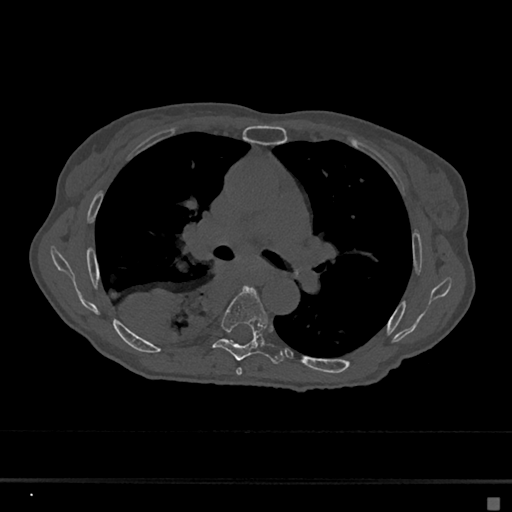
CT including the spine, one axial slice; slice 421 of 797 in the series (ordered by position); reconstruction kernel Br40s/3; 120 kVp; bone window (W 1800 / L 400 HU); 0.5 mm slice thickness; 512 × 512 image matrix, field of view 360 × 360 mm. Female patient, age 68 years. From the clinical record (not read from this slice): primary cancer: renal.
Structures marked on this image (semi-automatic segmentation, software-assisted and operator-edited):
- T5 vertebra: bounding box (x1, y1, x2, y2) in pixels: (236, 287, 255, 375)
- T6 vertebra: (212, 286, 284, 363)